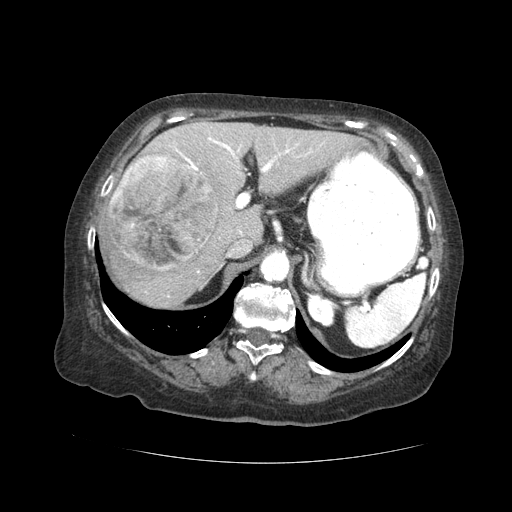
Contrast-enhanced abdominal CT (liver protocol), one axial slice; position 27 of 59 along the scan axis; 120 kVp; soft-tissue window (W 400 / L 40 HU); 2.5 mm slice thickness; 512 × 512 image matrix, field of view 380 × 380 mm. Case-level facts recorded for this patient, not image findings: diagnosis: hepatocellular carcinoma (patient treated with transarterial chemoembolisation; whether this scan precedes or follows treatment is not stated here); TNM stage (as recorded): Stage-I; Child-Pugh class: A; tumour nodularity: uninodular.
Annotated regions visible in this slice (semi-automatic segmentation, software-assisted and operator-edited):
- liver parenchyma outside the tumour (the mass and vessels are separate outlines, so this box may not span the whole liver): bounding box [x1, y1, x2, y2] px = [98, 120, 358, 306]
- mass: [110, 155, 218, 271]
- liver vessels: [174, 137, 324, 272]